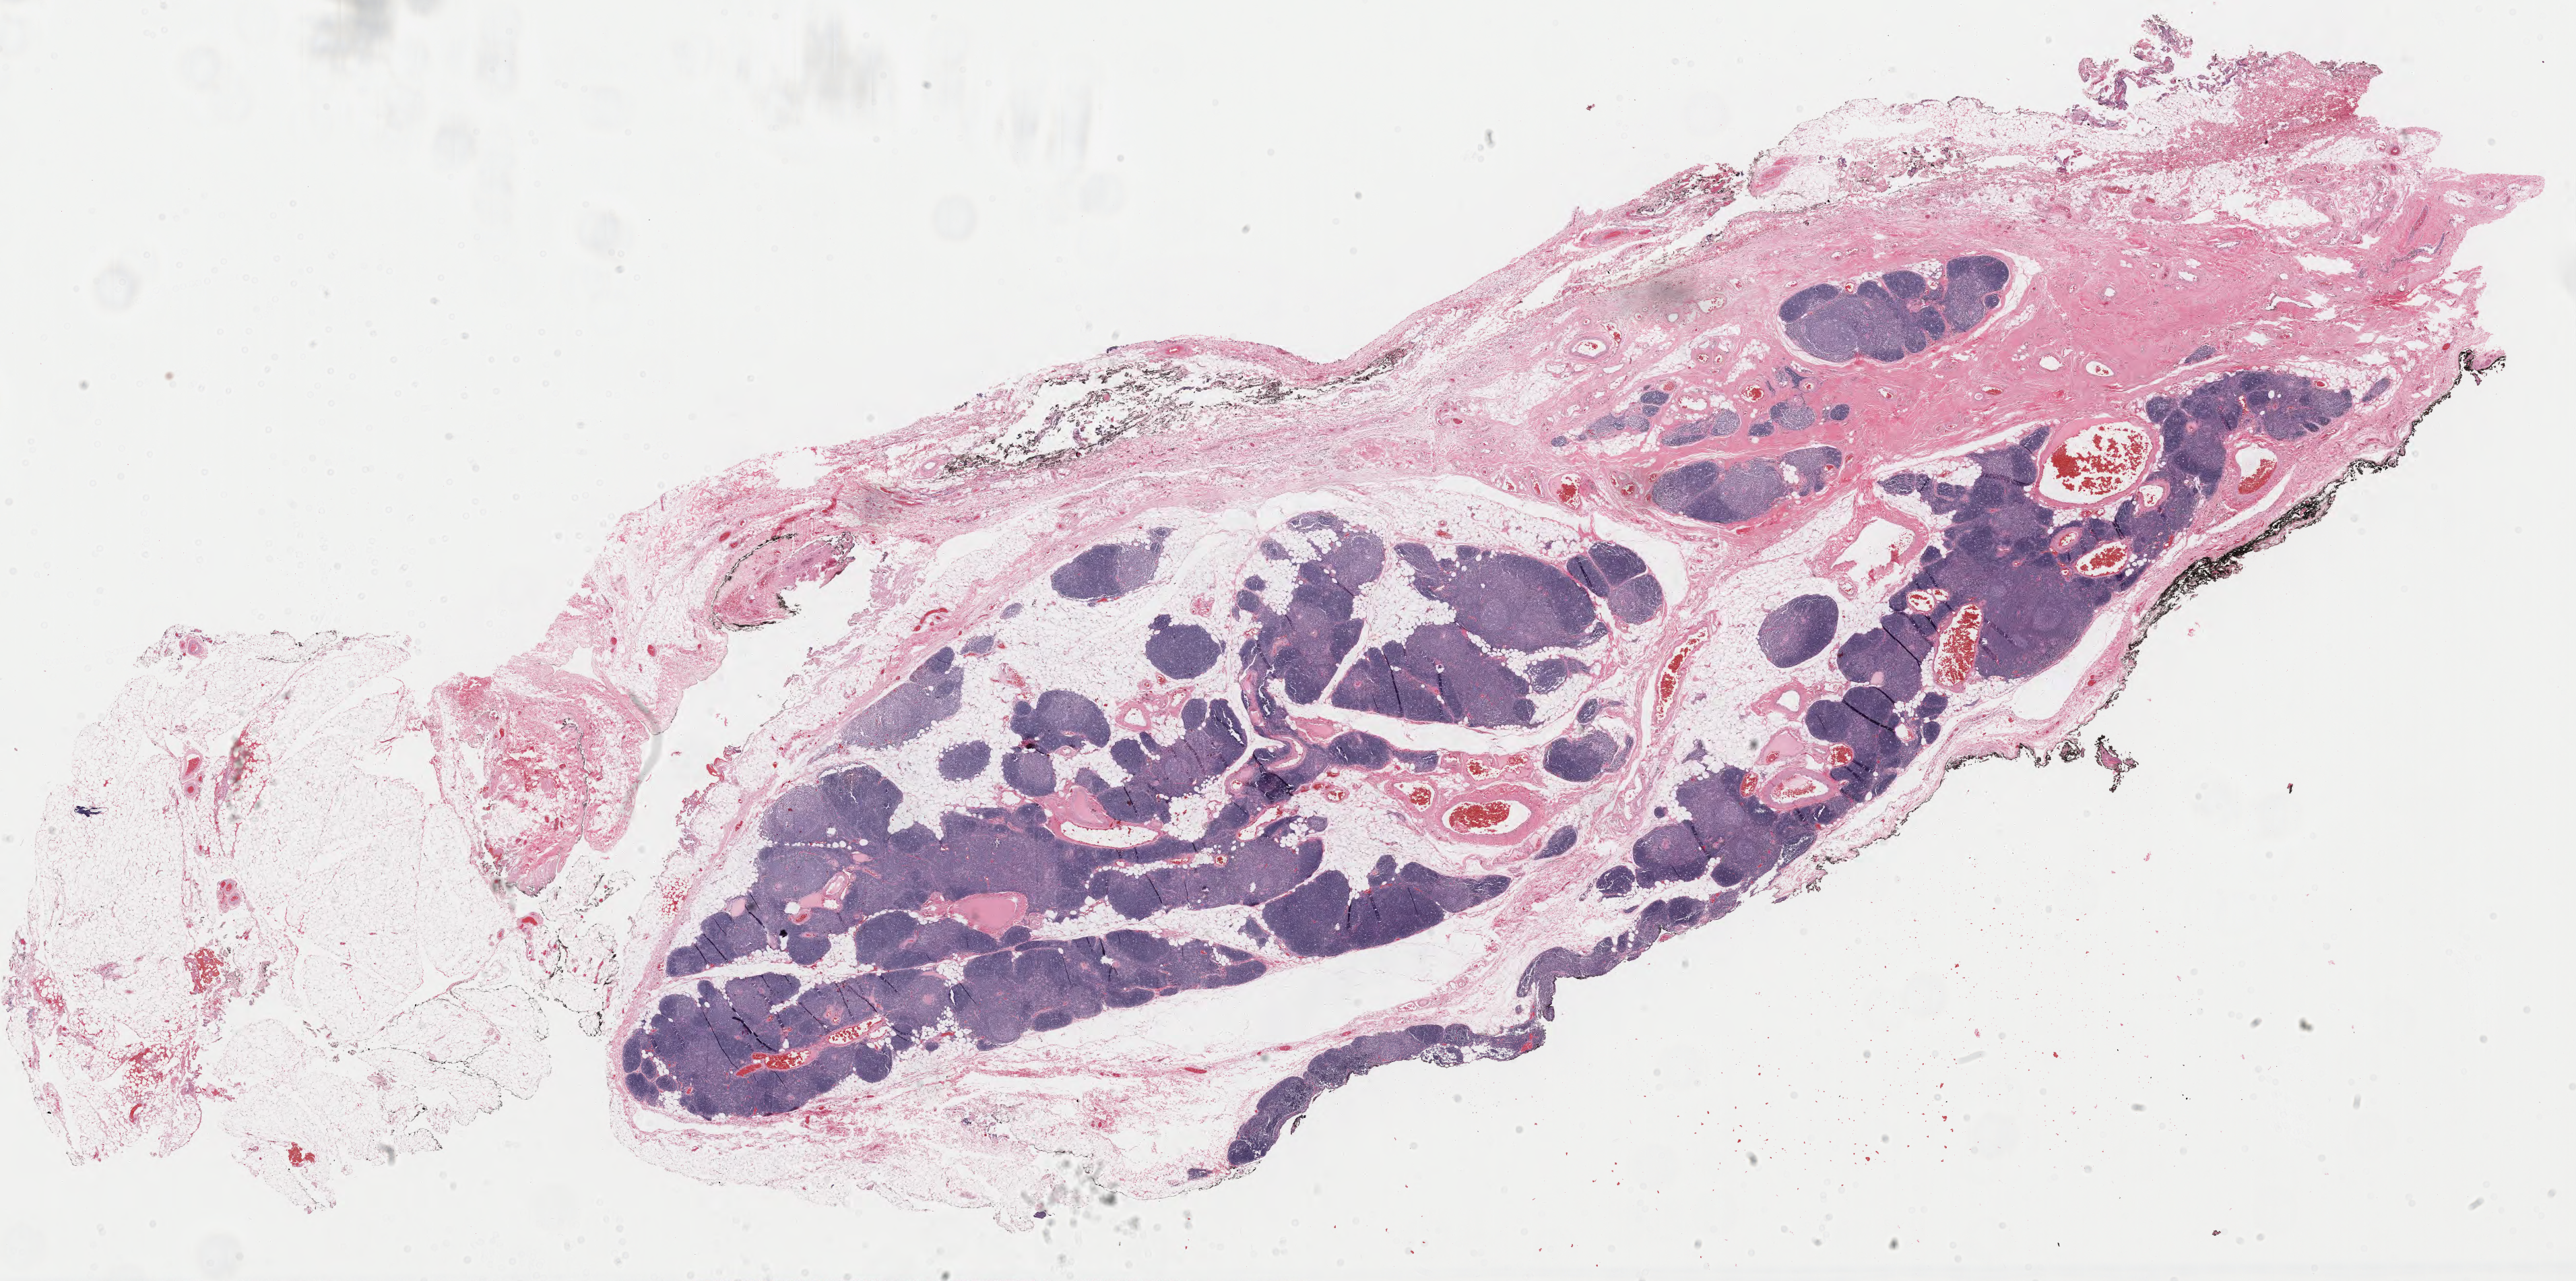
Digitized H&E-stained tissue section (whole slide), shown as a low-resolution overview of the whole scanned area (about 30.3 x 15.1 mm, acquisition: 40x scan). Formalin-fixed paraffin-embedded (FFPE) diagnostic section. Thymus, primary tumour sample. Female patient; age at initial diagnosis 43 years.
* histologic diagnosis: Thymoma, type B2, malignant